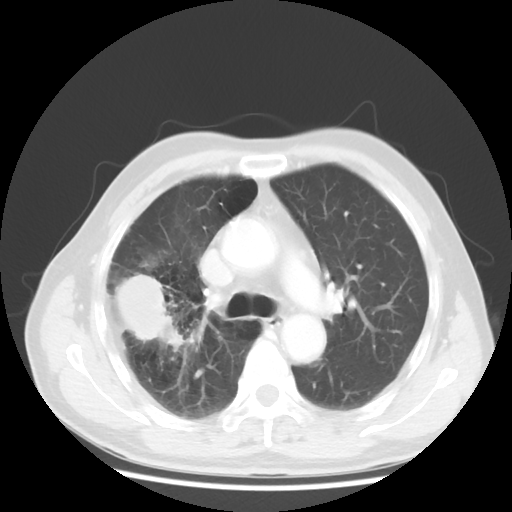
Chest CT, one axial slice; position 32 of 50 along the scan axis; lung window (W 1500 / L -600 HU); 5 mm slice thickness; 512 × 512 image matrix, field of view 360 × 360 mm. Male patient, age 69 years. From the clinical record (not read from this slice): clinical TNM (as recorded): T3 N0 M0.
Annotated regions visible in this slice (rectangle marked by the reading radiologist):
- lung tumour (recorded histology: adenocarcinoma): bounding box [x1, y1, x2, y2] px = [113, 268, 188, 353]